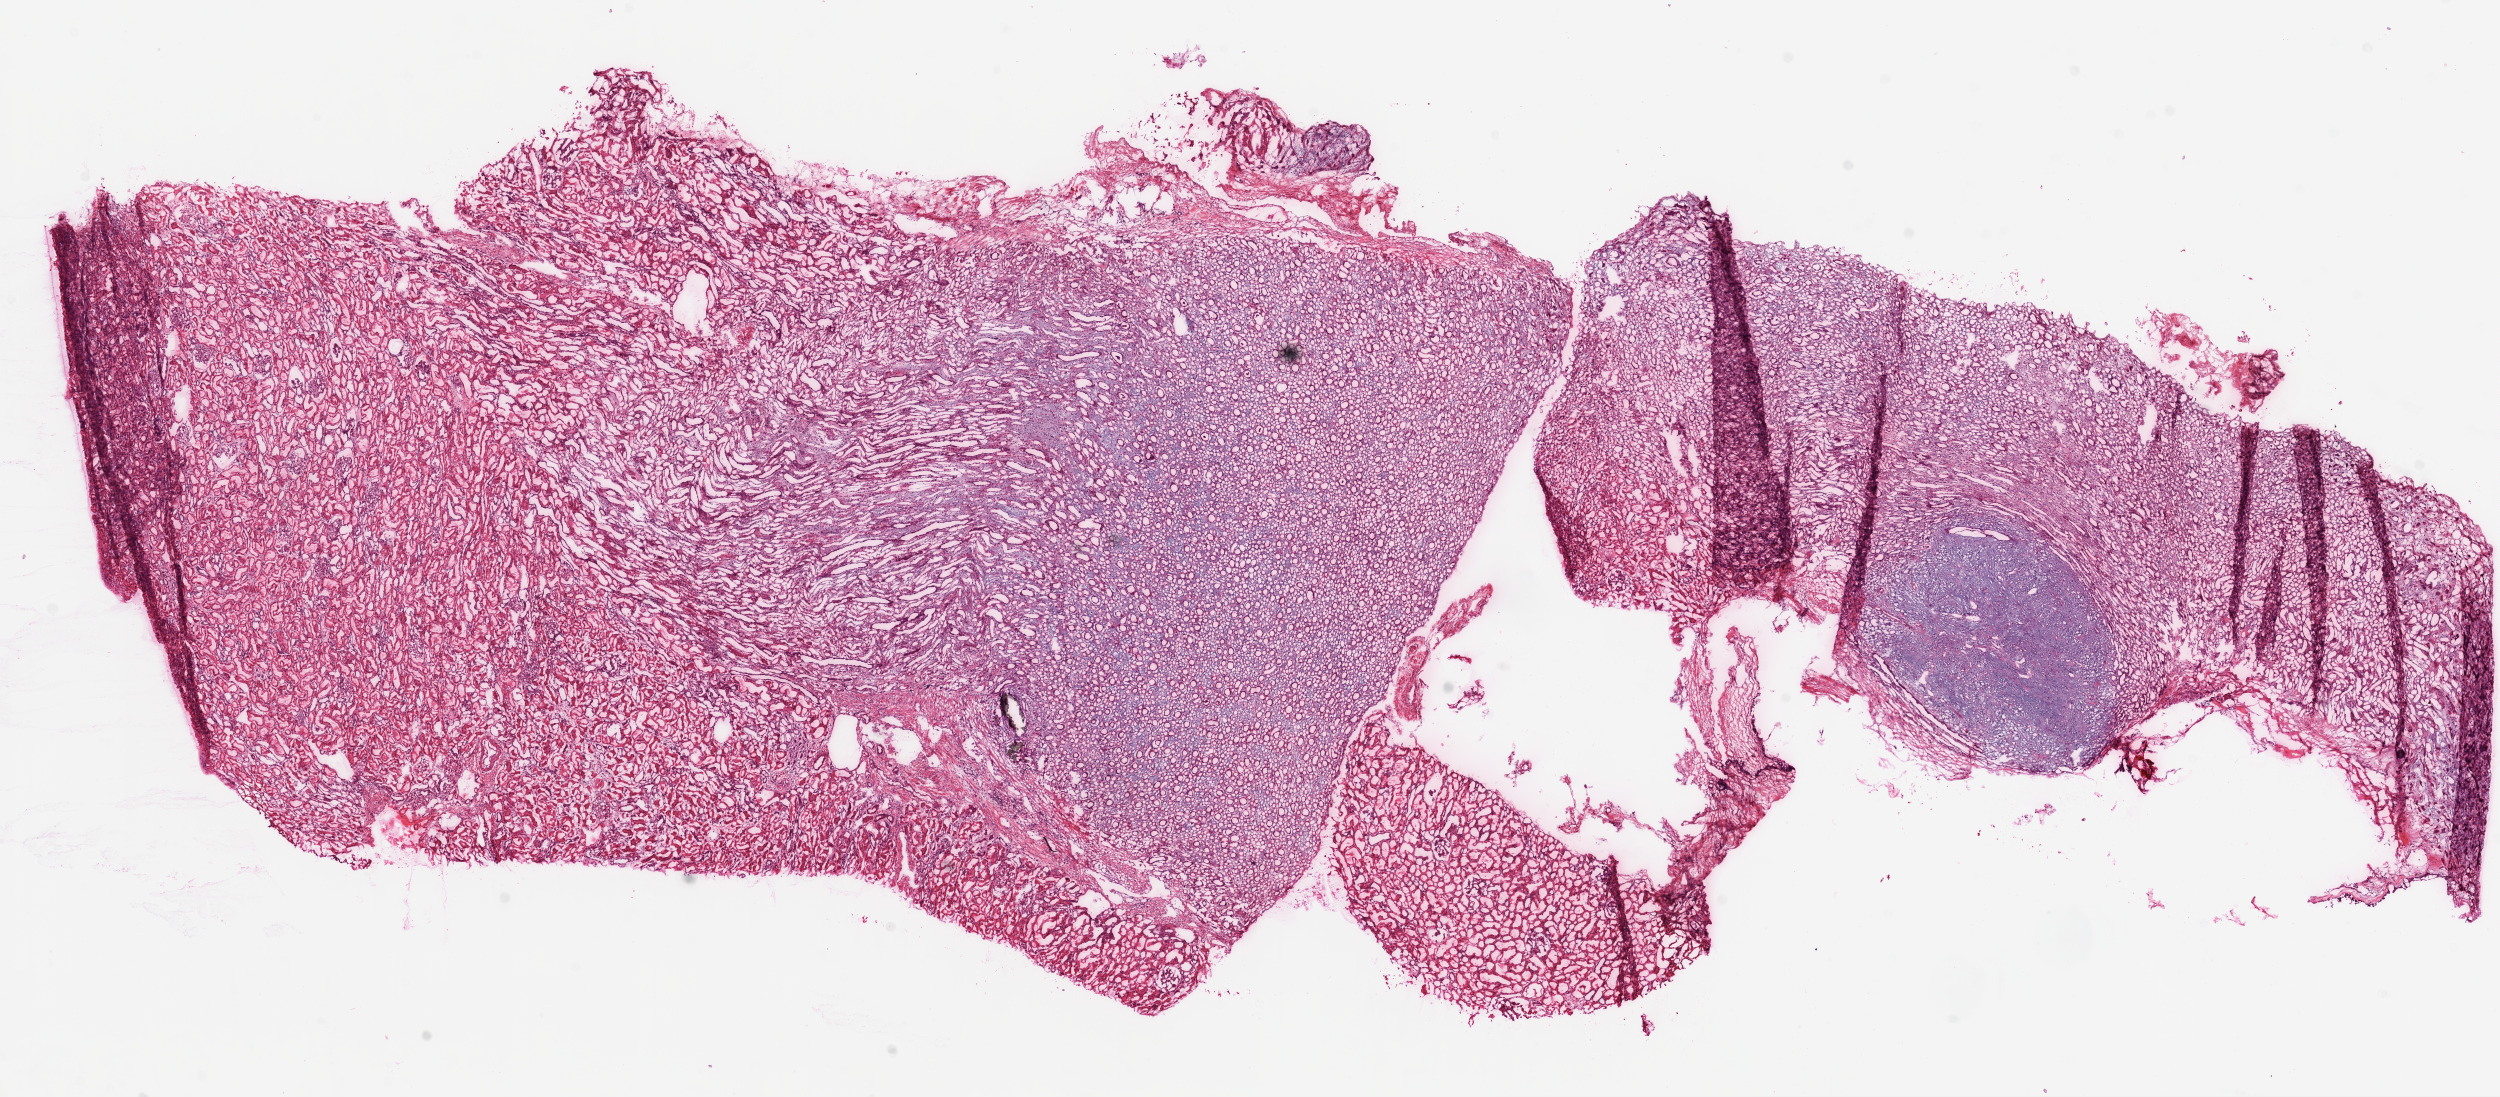
Digitized Hematoxylin and eosin (H&E) stained tissue section (whole slide), a low-resolution overview of the entire scanned area, about 20.1 x 8.8 mm (from a 20x scan). Frozen section from the top of the tissue portion. Sample: solid tissue normal (non-tumour tissue), kidney. Patient: male, age at initial diagnosis 38 years.
This section: solid tissue normal sample (biorepository sample class). Patient diagnosis: Clear cell adenocarcinoma, NOS.